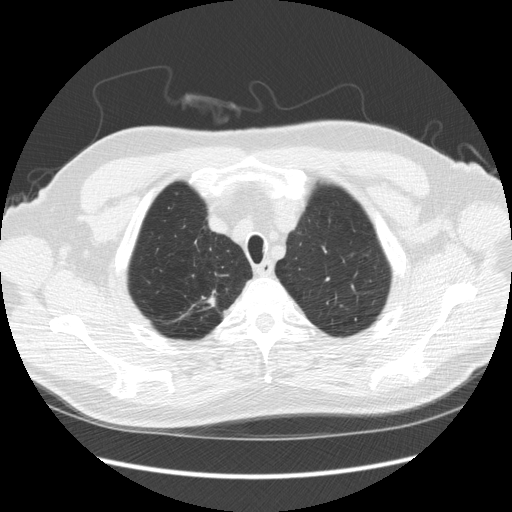
Low-dose screening chest CT, axial slice. Third annual screen. Lung window (W 1500 / L -600 HU). 2.5 mm slice thickness. Standard (soft-tissue) reconstruction kernel (STANDARD). Male, age 64 years at enrolment. Former smoker at enrolment.
Expert reader's lesion annotation, bounding box [x1, y1, x2, y2] px = [184, 285, 227, 321]. The screening reader recorded 4 non-calcified nodules or masses ≥4 mm on this exam (right upper lobe, right upper lobe, right upper lobe, right upper lobe); which of them this box marks is not recorded. Participant outcome: lung cancer diagnosed 15 days after this screen — adenocarcinoma, NOS, right upper lobe, moderately differentiated (G2), stage IA (AJCC 6th edition), 14 mm at pathology.